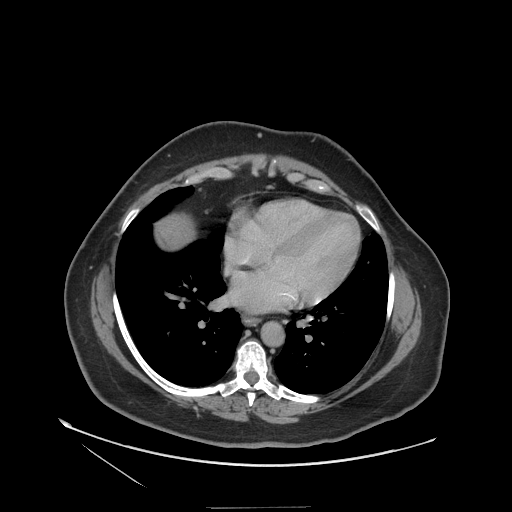
Contrast-enhanced abdominal CT (liver protocol), one axial slice. Slice 113 of 127 in the series (ordered by position). 140 kVp. Soft-tissue window (W 400 / L 40 HU). 2.5 mm slice thickness. 512 × 512 image matrix, field of view 480 × 480 mm. Case-level facts recorded for this patient, not image findings: diagnosis: hepatocellular carcinoma (patient treated with transarterial chemoembolisation; whether this scan precedes or follows treatment is not stated here); TNM stage (as recorded): Stage-II; Child-Pugh class: A; tumour differentiation: well differentiated; tumour size: 3 cm.
Outlined on this slice (semi-automatic segmentation, software-assisted and operator-edited):
- liver parenchyma outside the tumour (the mass and vessels are separate outlines, so this box may not span the whole liver): bounding box (x1, y1, x2, y2) in pixels: (156, 218, 184, 244)